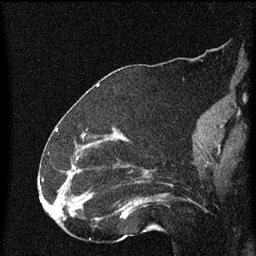
Breast MRI (dynamic contrast-enhanced), one sagittal slice; dynamic contrast-enhanced series, image 2 of 4 at this slice position (ordered by acquisition); 1.5 T; TE 4.2 ms, TR 8 ms; 2 mm slice thickness; 256 × 256 image matrix, field of view 180 × 180 mm. Patient: female, 52 years.
Annotated regions visible in this slice (semi-automatically segmented with operator editing):
- analysis volume of interest (the breast-tissue region the enhancement analysis was run in; not a lesion): bounding box [x1, y1, x2, y2] px = [73, 148, 172, 219]
- tumour enhancement mask (voxels above the 70 % enhancement threshold inside the analysis volume of interest): [73, 158, 132, 217]